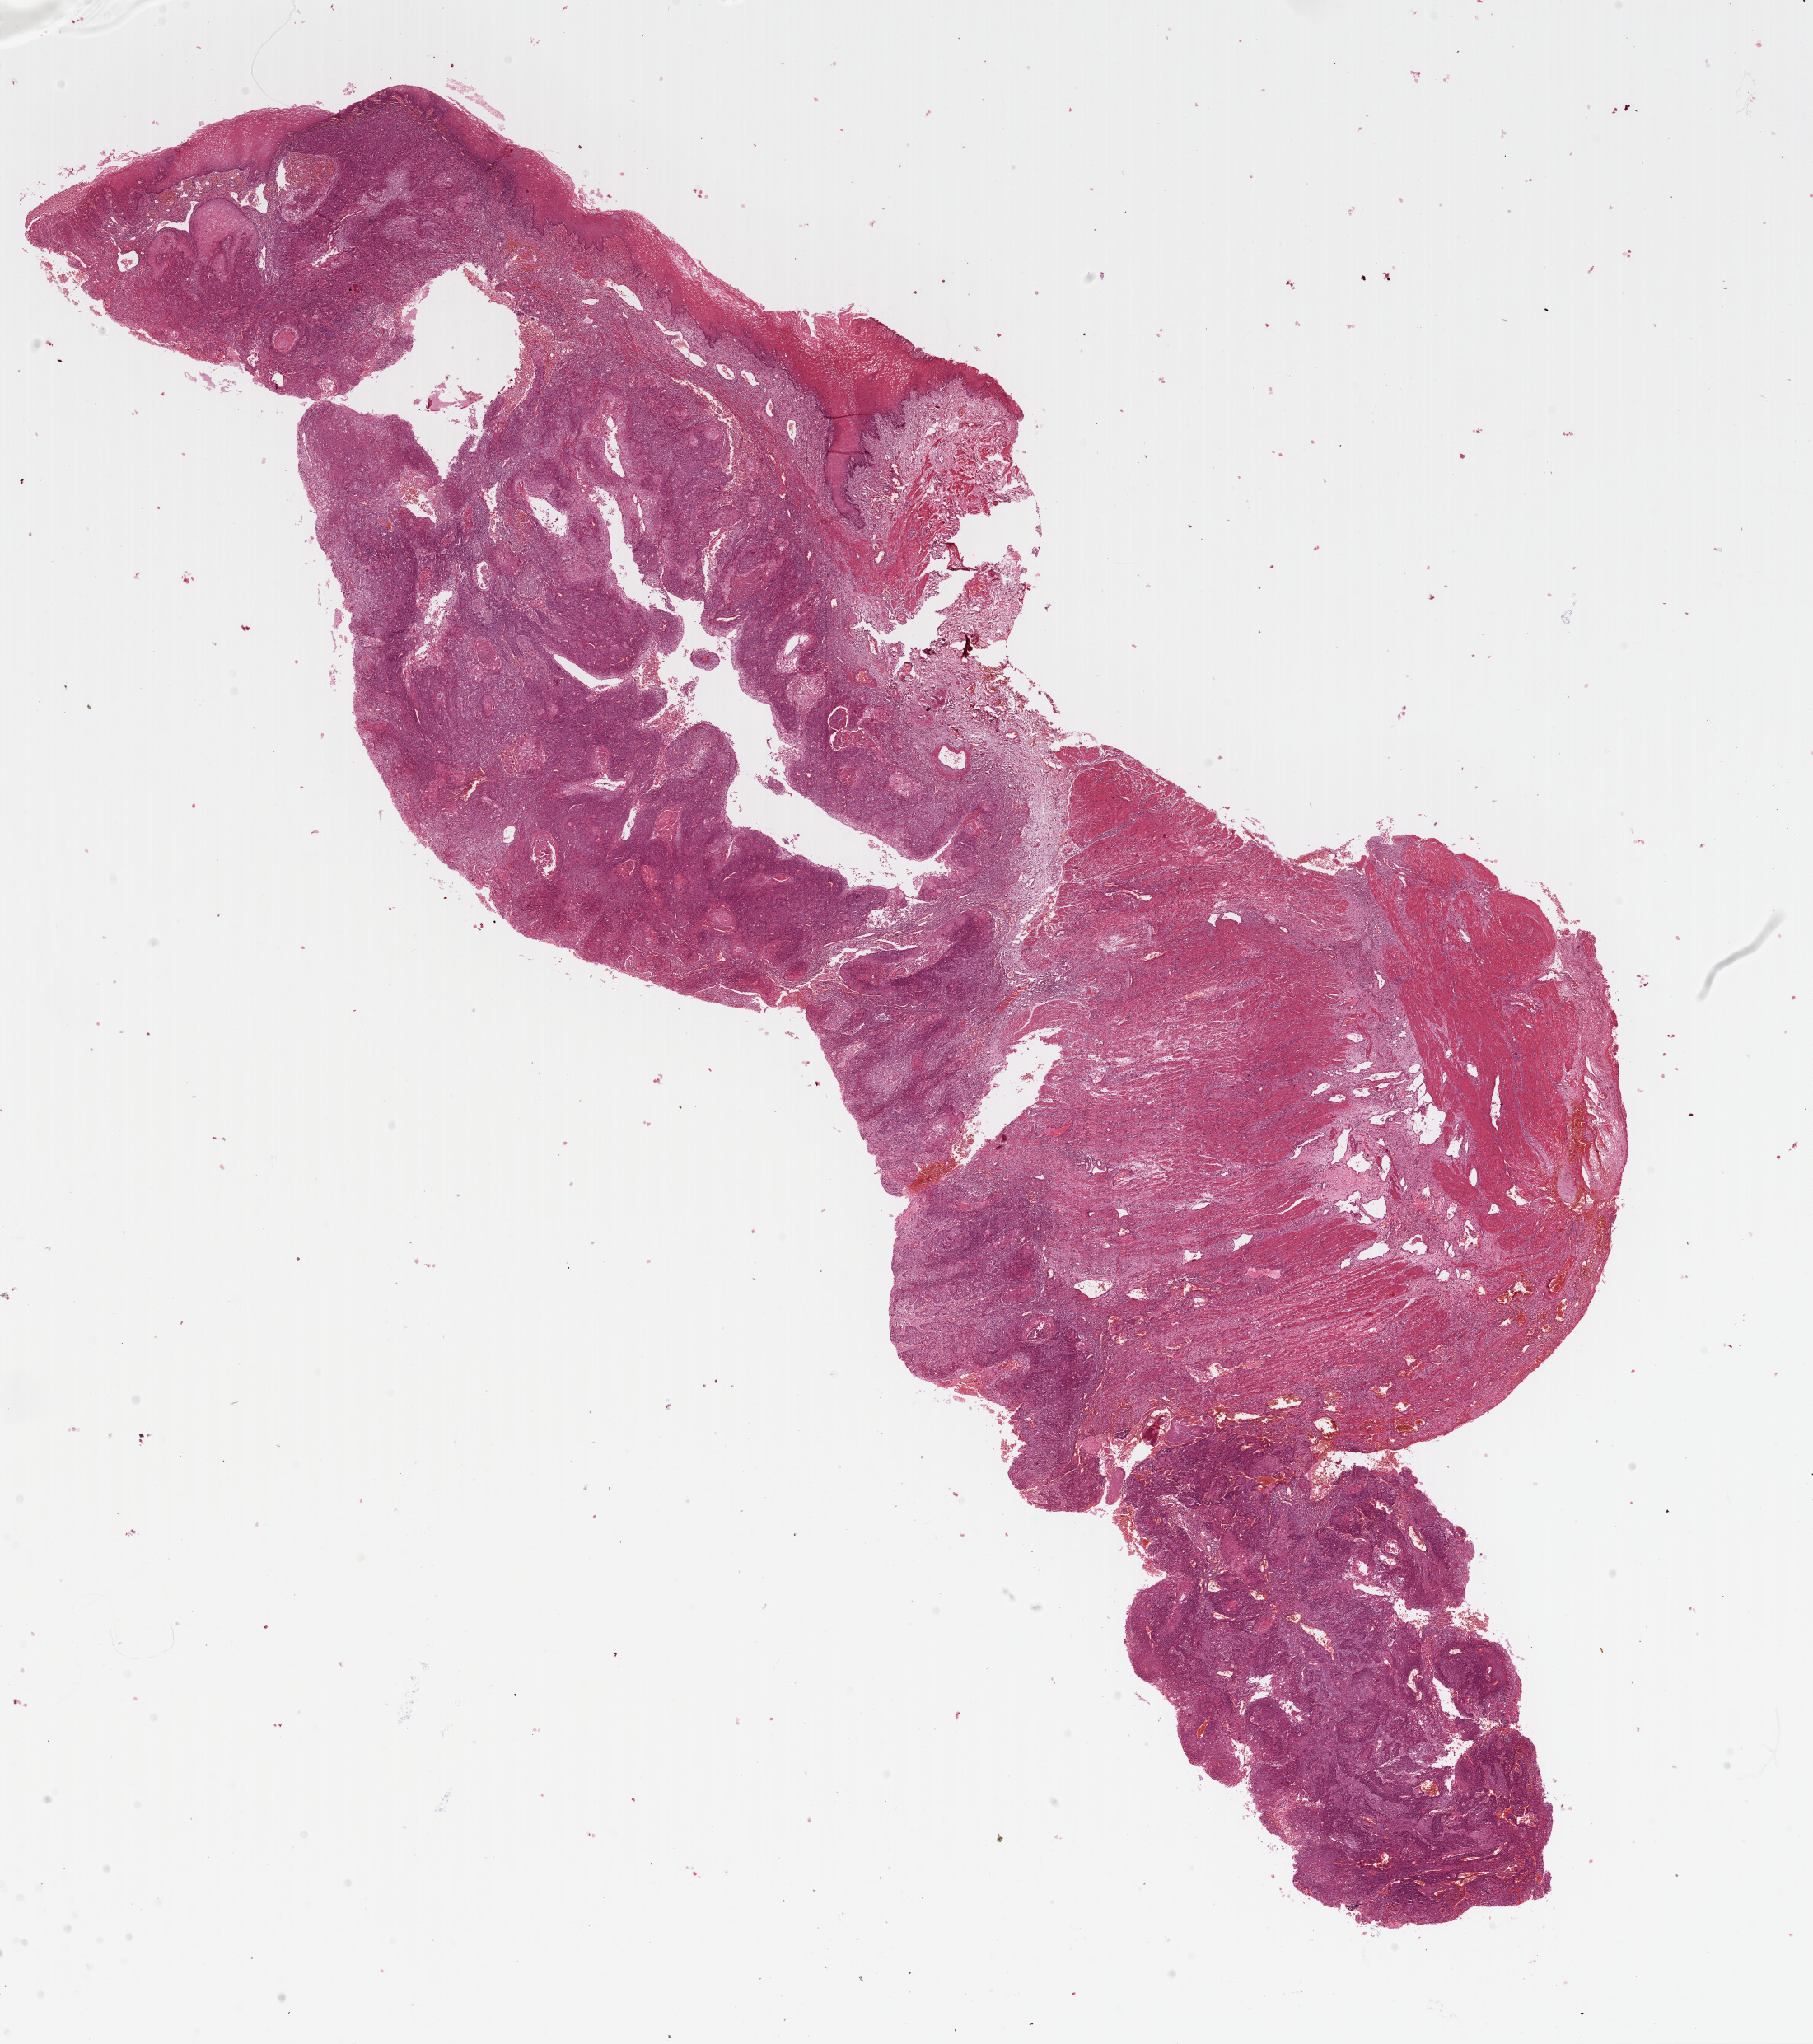
Hematoxylin and eosin (H&E) stained whole-slide image, whole scanned area (about 17.4 x 19.6 mm, slide scanned at 40x) shown as a low-resolution overview, FFPE section, sample: primary tumour, esophagus. Male, age 57 years at initial diagnosis. Histologic grade: G2 (moderately differentiated).
• AJCC pathologic stage: IIA (6th edition)
• histologic diagnosis: Squamous cell carcinoma, NOS